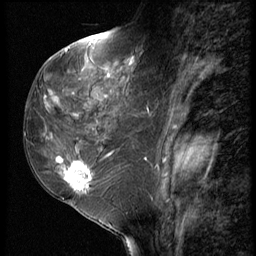
Breast MRI (dynamic contrast-enhanced), one sagittal slice; slice 28 of 62 in the series (ordered by position); 3 images stored at this slice position (order not interpretable as contrast timing); 1.5 T; TE 4.2 ms, TR 9 ms; 2.5 mm slice thickness; 256 × 256 image matrix, field of view 180 × 180 mm. Patient: female, 50 years. Case-level facts recorded for this patient, not image findings: setting: breast cancer imaged before/during neoadjuvant chemotherapy; receptor status: HR-positive, HER2-negative.
Outlined on this slice (semi-automatic segmentation, software-assisted and operator-edited):
- analysis volume of interest (the breast-tissue region the enhancement analysis was run in; not a lesion): bounding box <32,91,118,209> (left, top, right, bottom; pixels)
- tumour enhancement mask (voxels above the 140 % enhancement threshold inside the analysis volume of interest): <58,156,108,190>